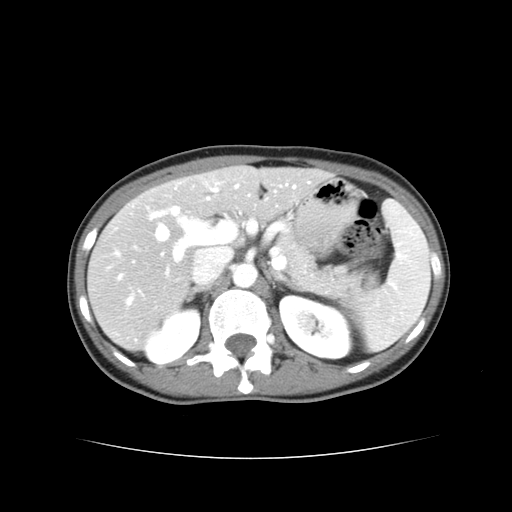
Contrast-enhanced abdominal CT, one axial slice. Slice 22 of 38 in the series (ordered by position). 120 kVp. Intravenous contrast given. Soft-tissue window (W 400 / L 40 HU). 5 mm slice thickness. 512 × 512 image matrix, field of view 340 × 340 mm. Female patient, age 54 years. Case-level facts recorded for this patient, not image findings: diagnosis: colorectal cancer liver metastases, imaged before liver resection; multiple liver metastases: yes.
Annotated regions visible in this slice (outlined manually by an expert reader):
- hepatic veins: bounding box [x1, y1, x2, y2] px = [119, 186, 296, 279]
- liver: [89, 166, 326, 347]
- planned liver remnant (the part of the liver to remain after resection): [215, 166, 326, 218]
- portal vein (with intrahepatic branches): [151, 185, 239, 258]